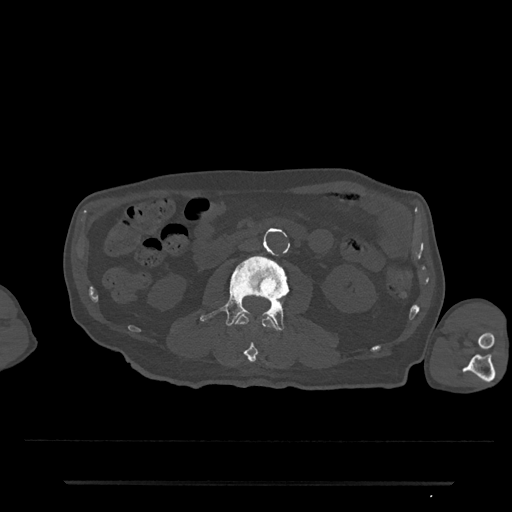
CT including the spine, one axial slice. Reconstruction kernel Br40s/3. 120 kVp. Bone window (W 1800 / L 400 HU). 0.5 mm slice thickness. 512 × 512 image matrix, field of view 427 × 427 mm. Patient: male, 74 years. Case-level facts recorded for this patient, not image findings: primary cancer: prostate.
Structures marked on this image (semi-automatically segmented with operator editing):
- L2 vertebra: box from (x=234, y=314) to (x=279, y=363) px
- L3 vertebra: (x=200, y=253)–(x=301, y=331)